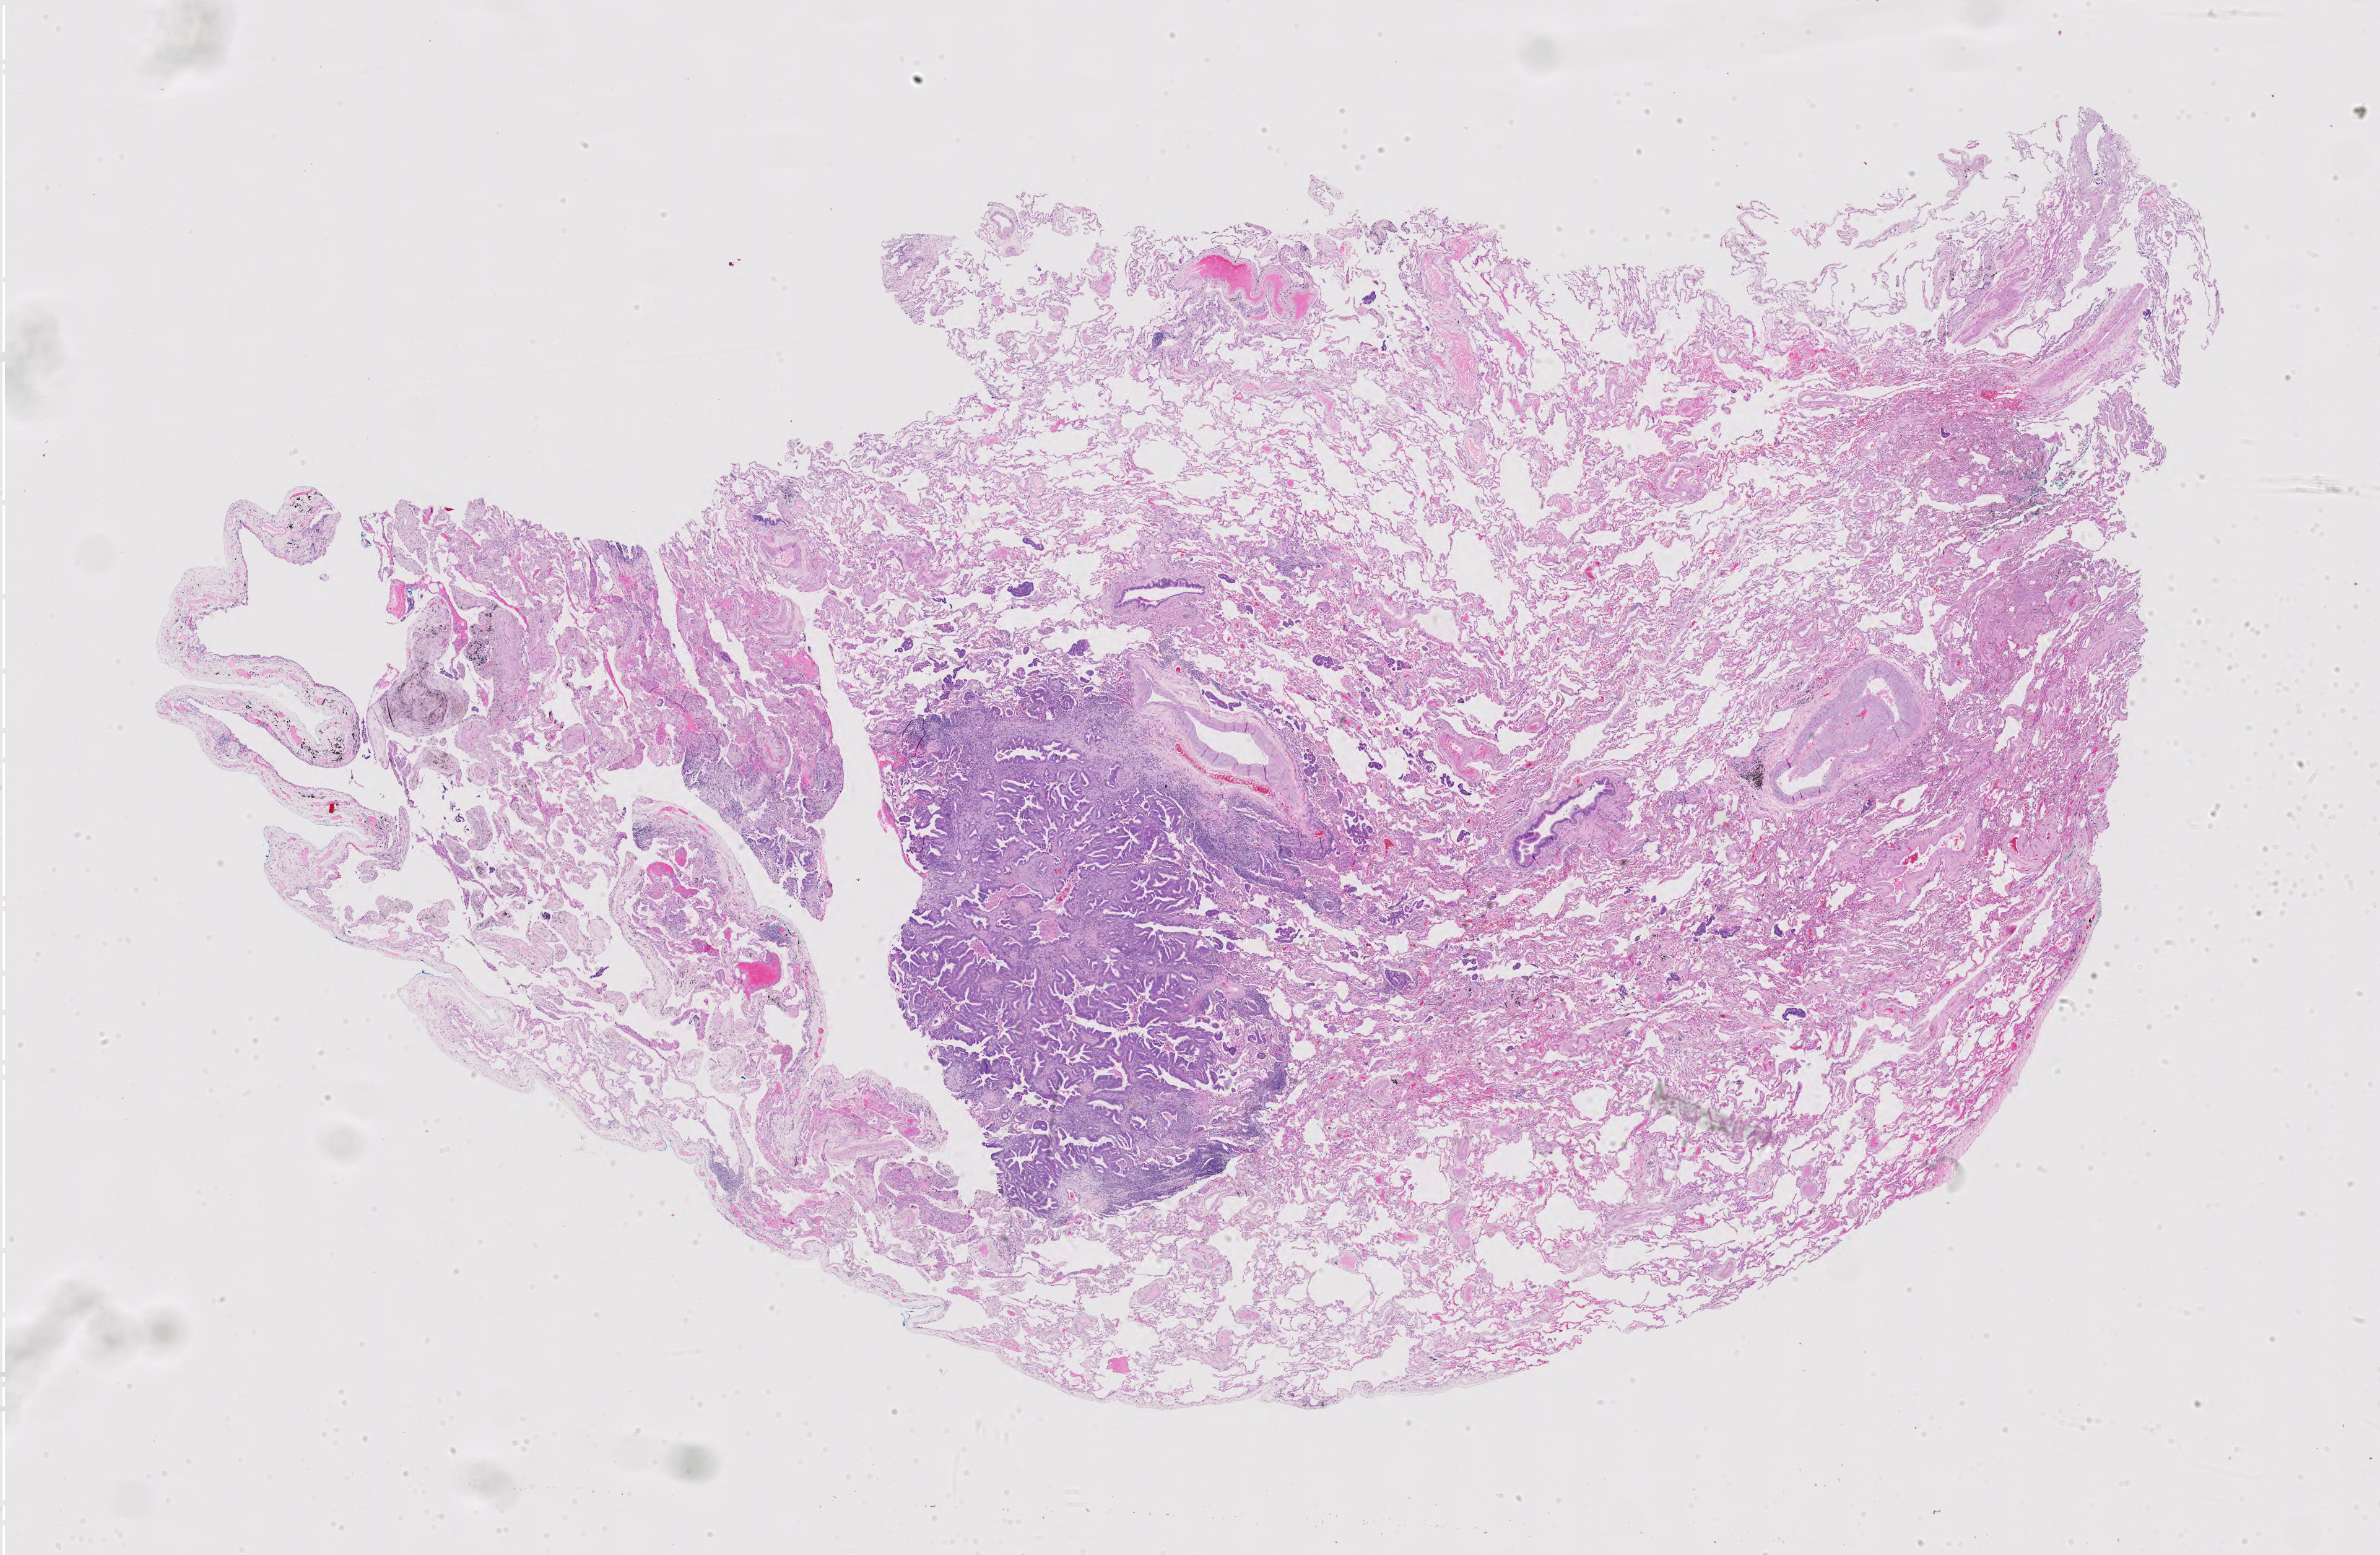
Whole-slide histology image, H&E-stained, shown as a low-resolution overview of the whole scanned area (about 27.9 x 18.2 mm), FFPE section, sample: primary tumour, lung. Male patient; age at initial diagnosis 67 years.
• pathologic diagnosis: Adenocarcinoma with mixed subtypes (upper lobe, lung)
• TNM: T1a N0 M0
• AJCC pathologic stage: IA (7th edition)